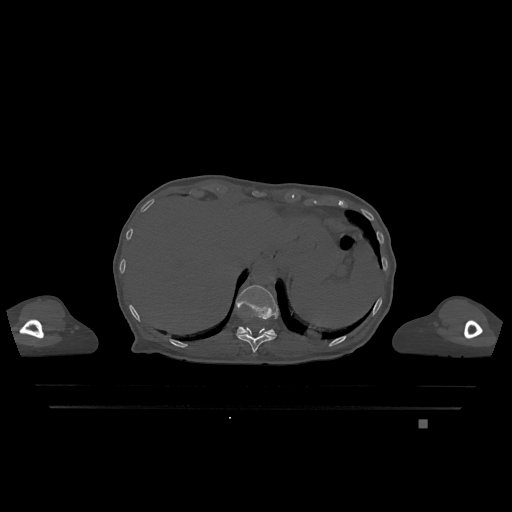
CT including the spine, one axial slice; position 566 of 1317 along the scan axis; bone window (W 1800 / L 400 HU); 0.5 mm slice thickness; 512 × 512 image matrix, field of view 500 × 500 mm. Female patient, age 74 years. From the clinical record (not read from this slice): primary cancer: lung.
Annotated regions visible in this slice (semi-automatically segmented with operator editing):
- T11 vertebra: box from (x=236, y=327) to (x=276, y=352) px
- T12 vertebra: (x=236, y=285)–(x=278, y=336)